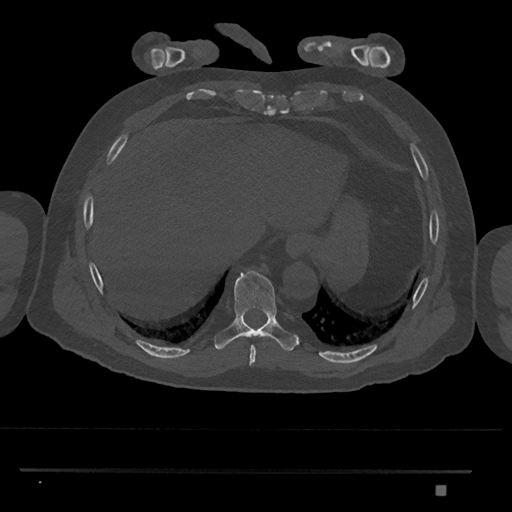
CT including the spine, one axial slice; position 1062 of 1134 along the scan axis; reconstruction kernel Br40s/3; 120 kVp; bone window (W 1800 / L 400 HU); 0.5 mm slice thickness; 512 × 512 image matrix. Patient: male, 65 years. Case-level facts recorded for this patient, not image findings: primary cancer: prostate.
Outlined on this slice (semi-automatically segmented with operator editing):
- T8 vertebra: box from (x=249, y=345) to (x=256, y=366) px
- T9 vertebra: (x=213, y=270)–(x=300, y=352)